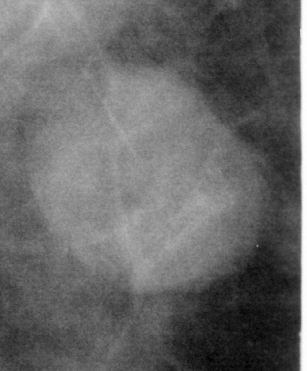
Region of interest cut from a scanned film mammogram (one marked finding), right breast, CC view.
- Finding: mass, shape oval, margins circumscribed; BI-RADS assessment category 3; pathology result (as recorded, not read from the image): benign.